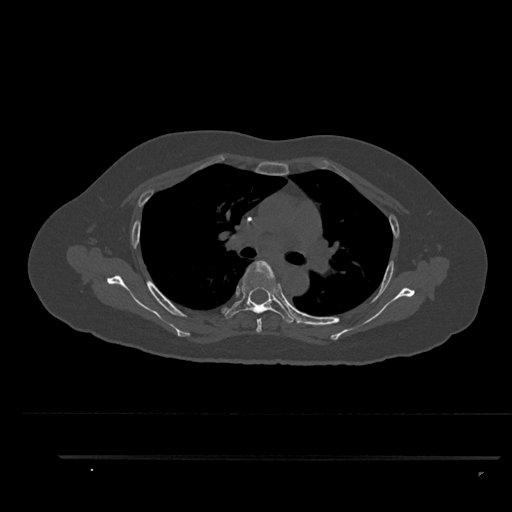
CT including the spine, one axial slice. Position 612 of 797 along the scan axis. Reconstruction kernel Br40s/3. 120 kVp. Bone window (W 1800 / L 400 HU). 512 × 512 image matrix, field of view 408 × 408 mm. Female patient, age 44 years. From the clinical record (not read from this slice): primary cancer: renal.
Annotated regions visible in this slice (semi-automatic segmentation, software-assisted and operator-edited):
- T4 vertebra: bounding box (x1, y1, x2, y2) in pixels: (256, 318, 262, 333)
- T5 vertebra: (222, 260, 296, 323)